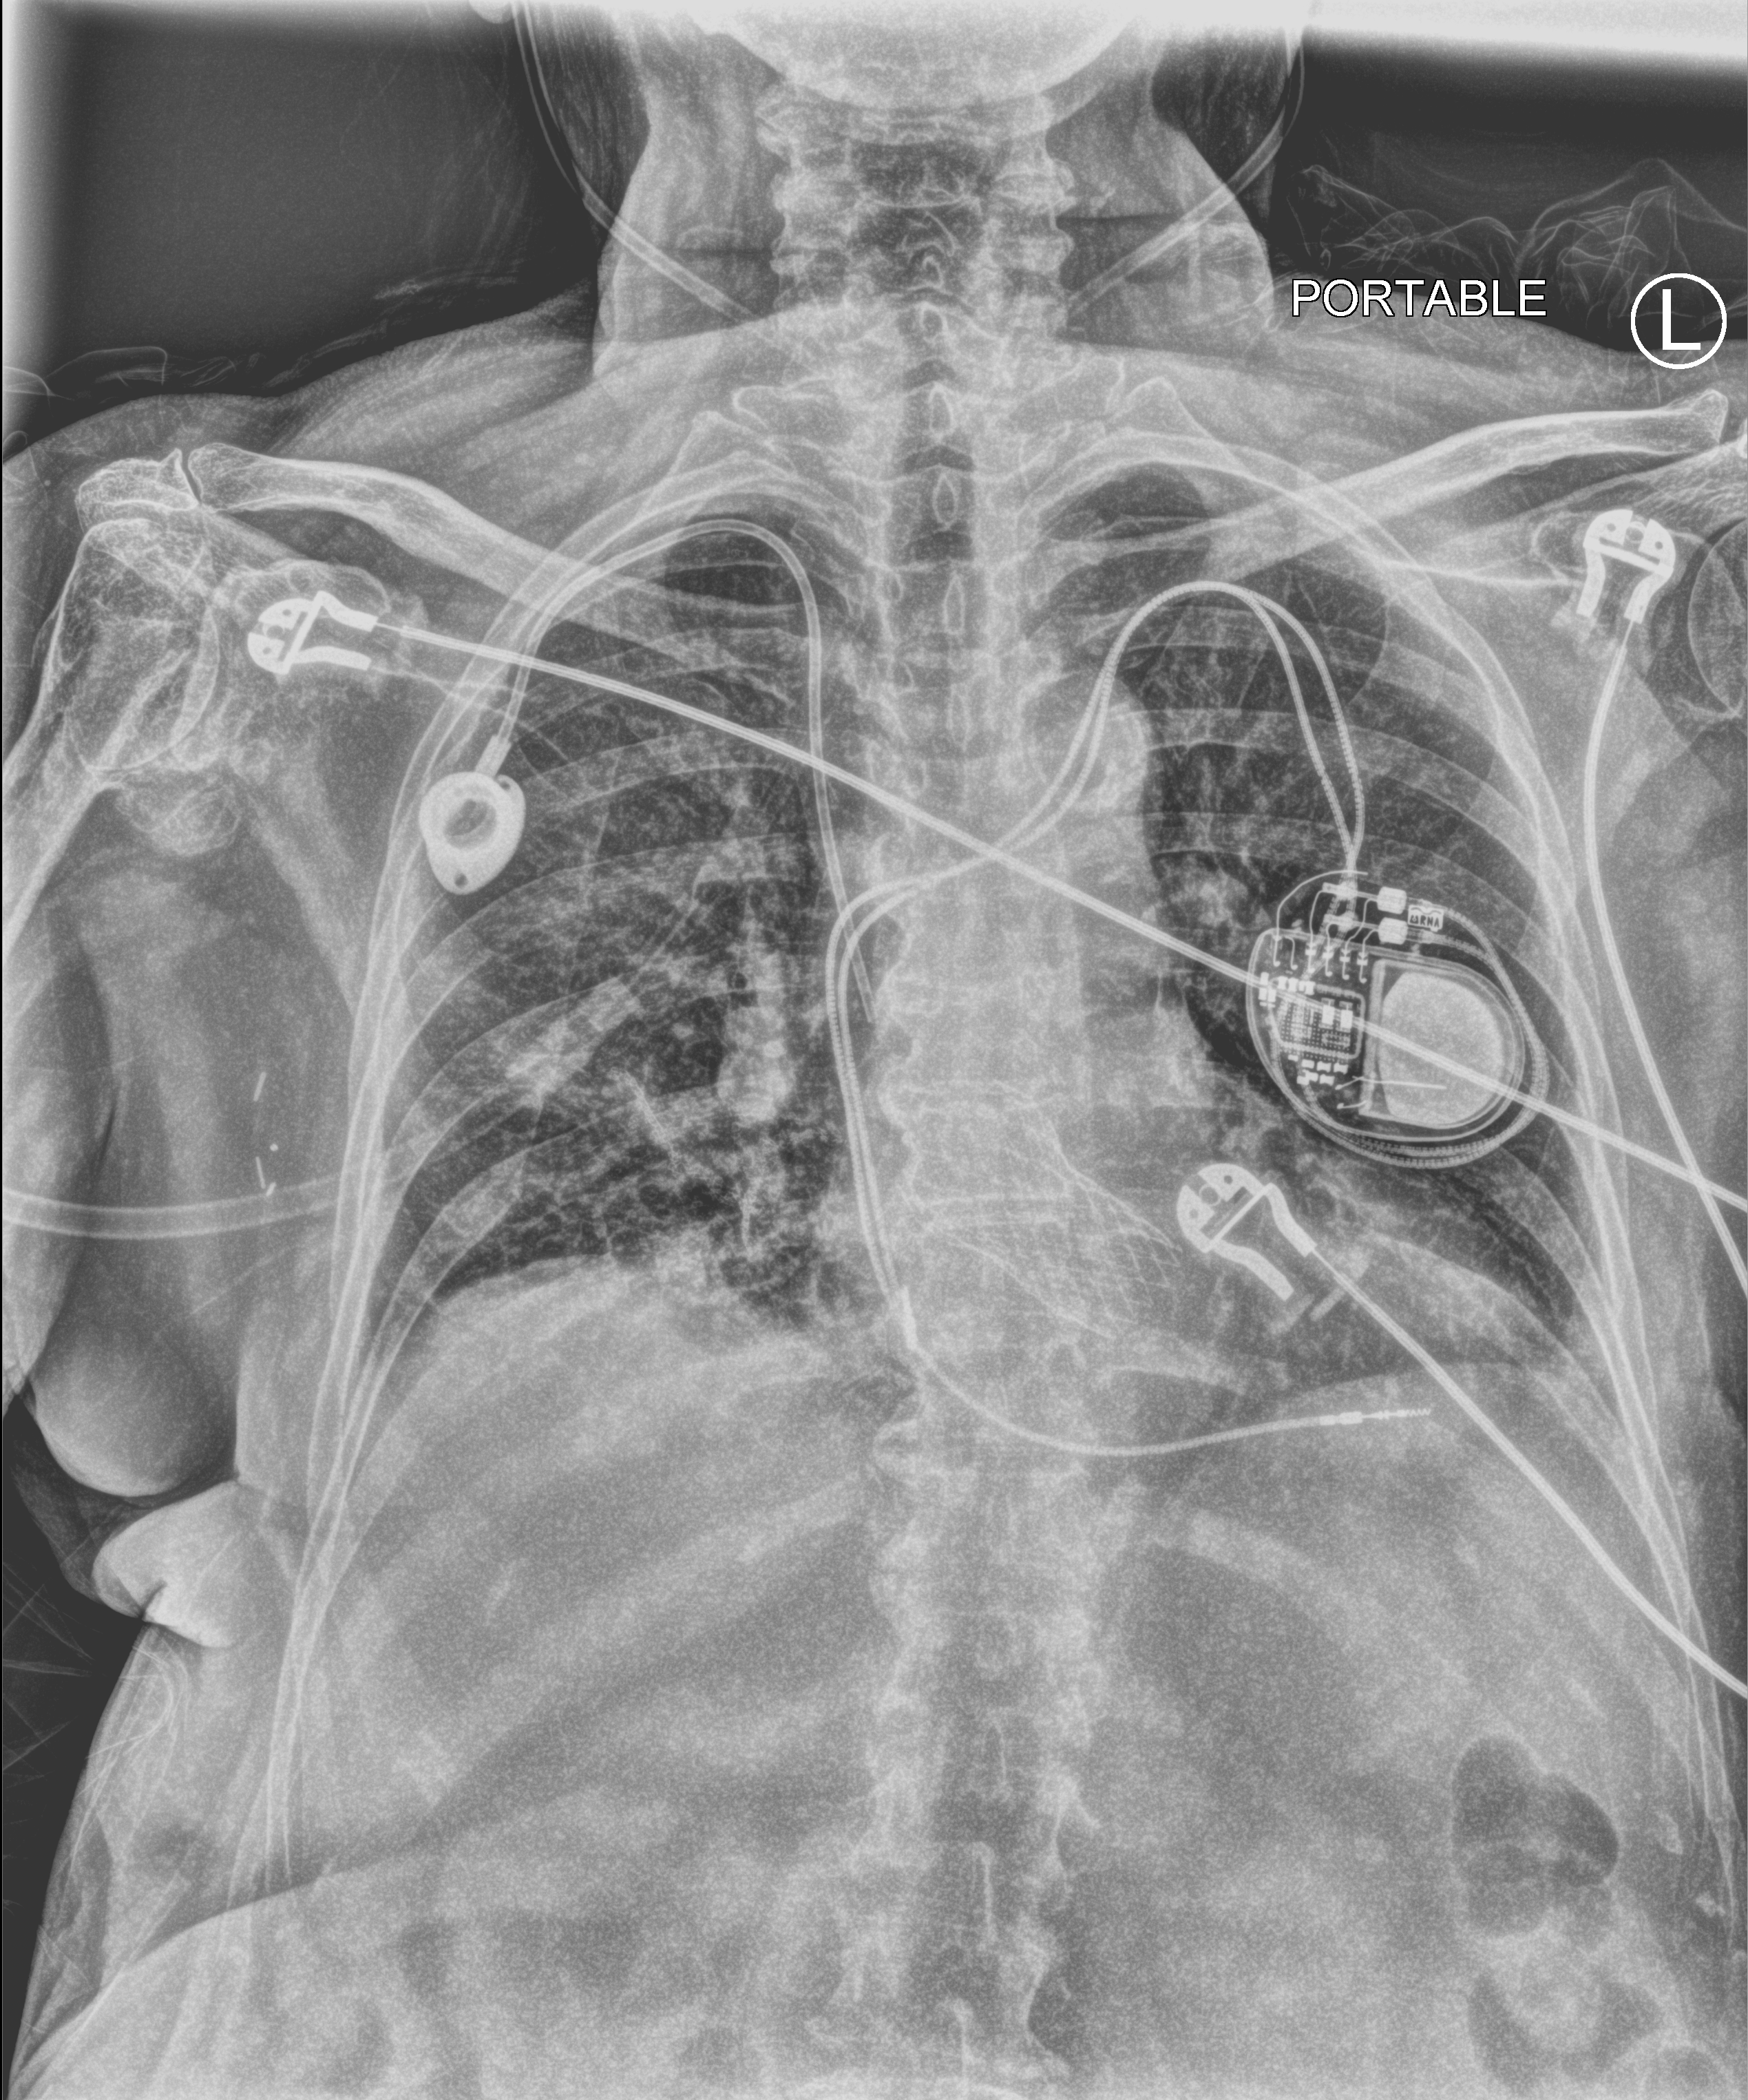
Chest X-ray (portable); anteroposterior (AP) projection. Patient hospitalised with COVID-19; female, aged 75–90 years.
From the hospital-stay record, not from the radiograph (when in the stay this image was taken is not recorded):
- mechanically ventilated during this hospital stay: no